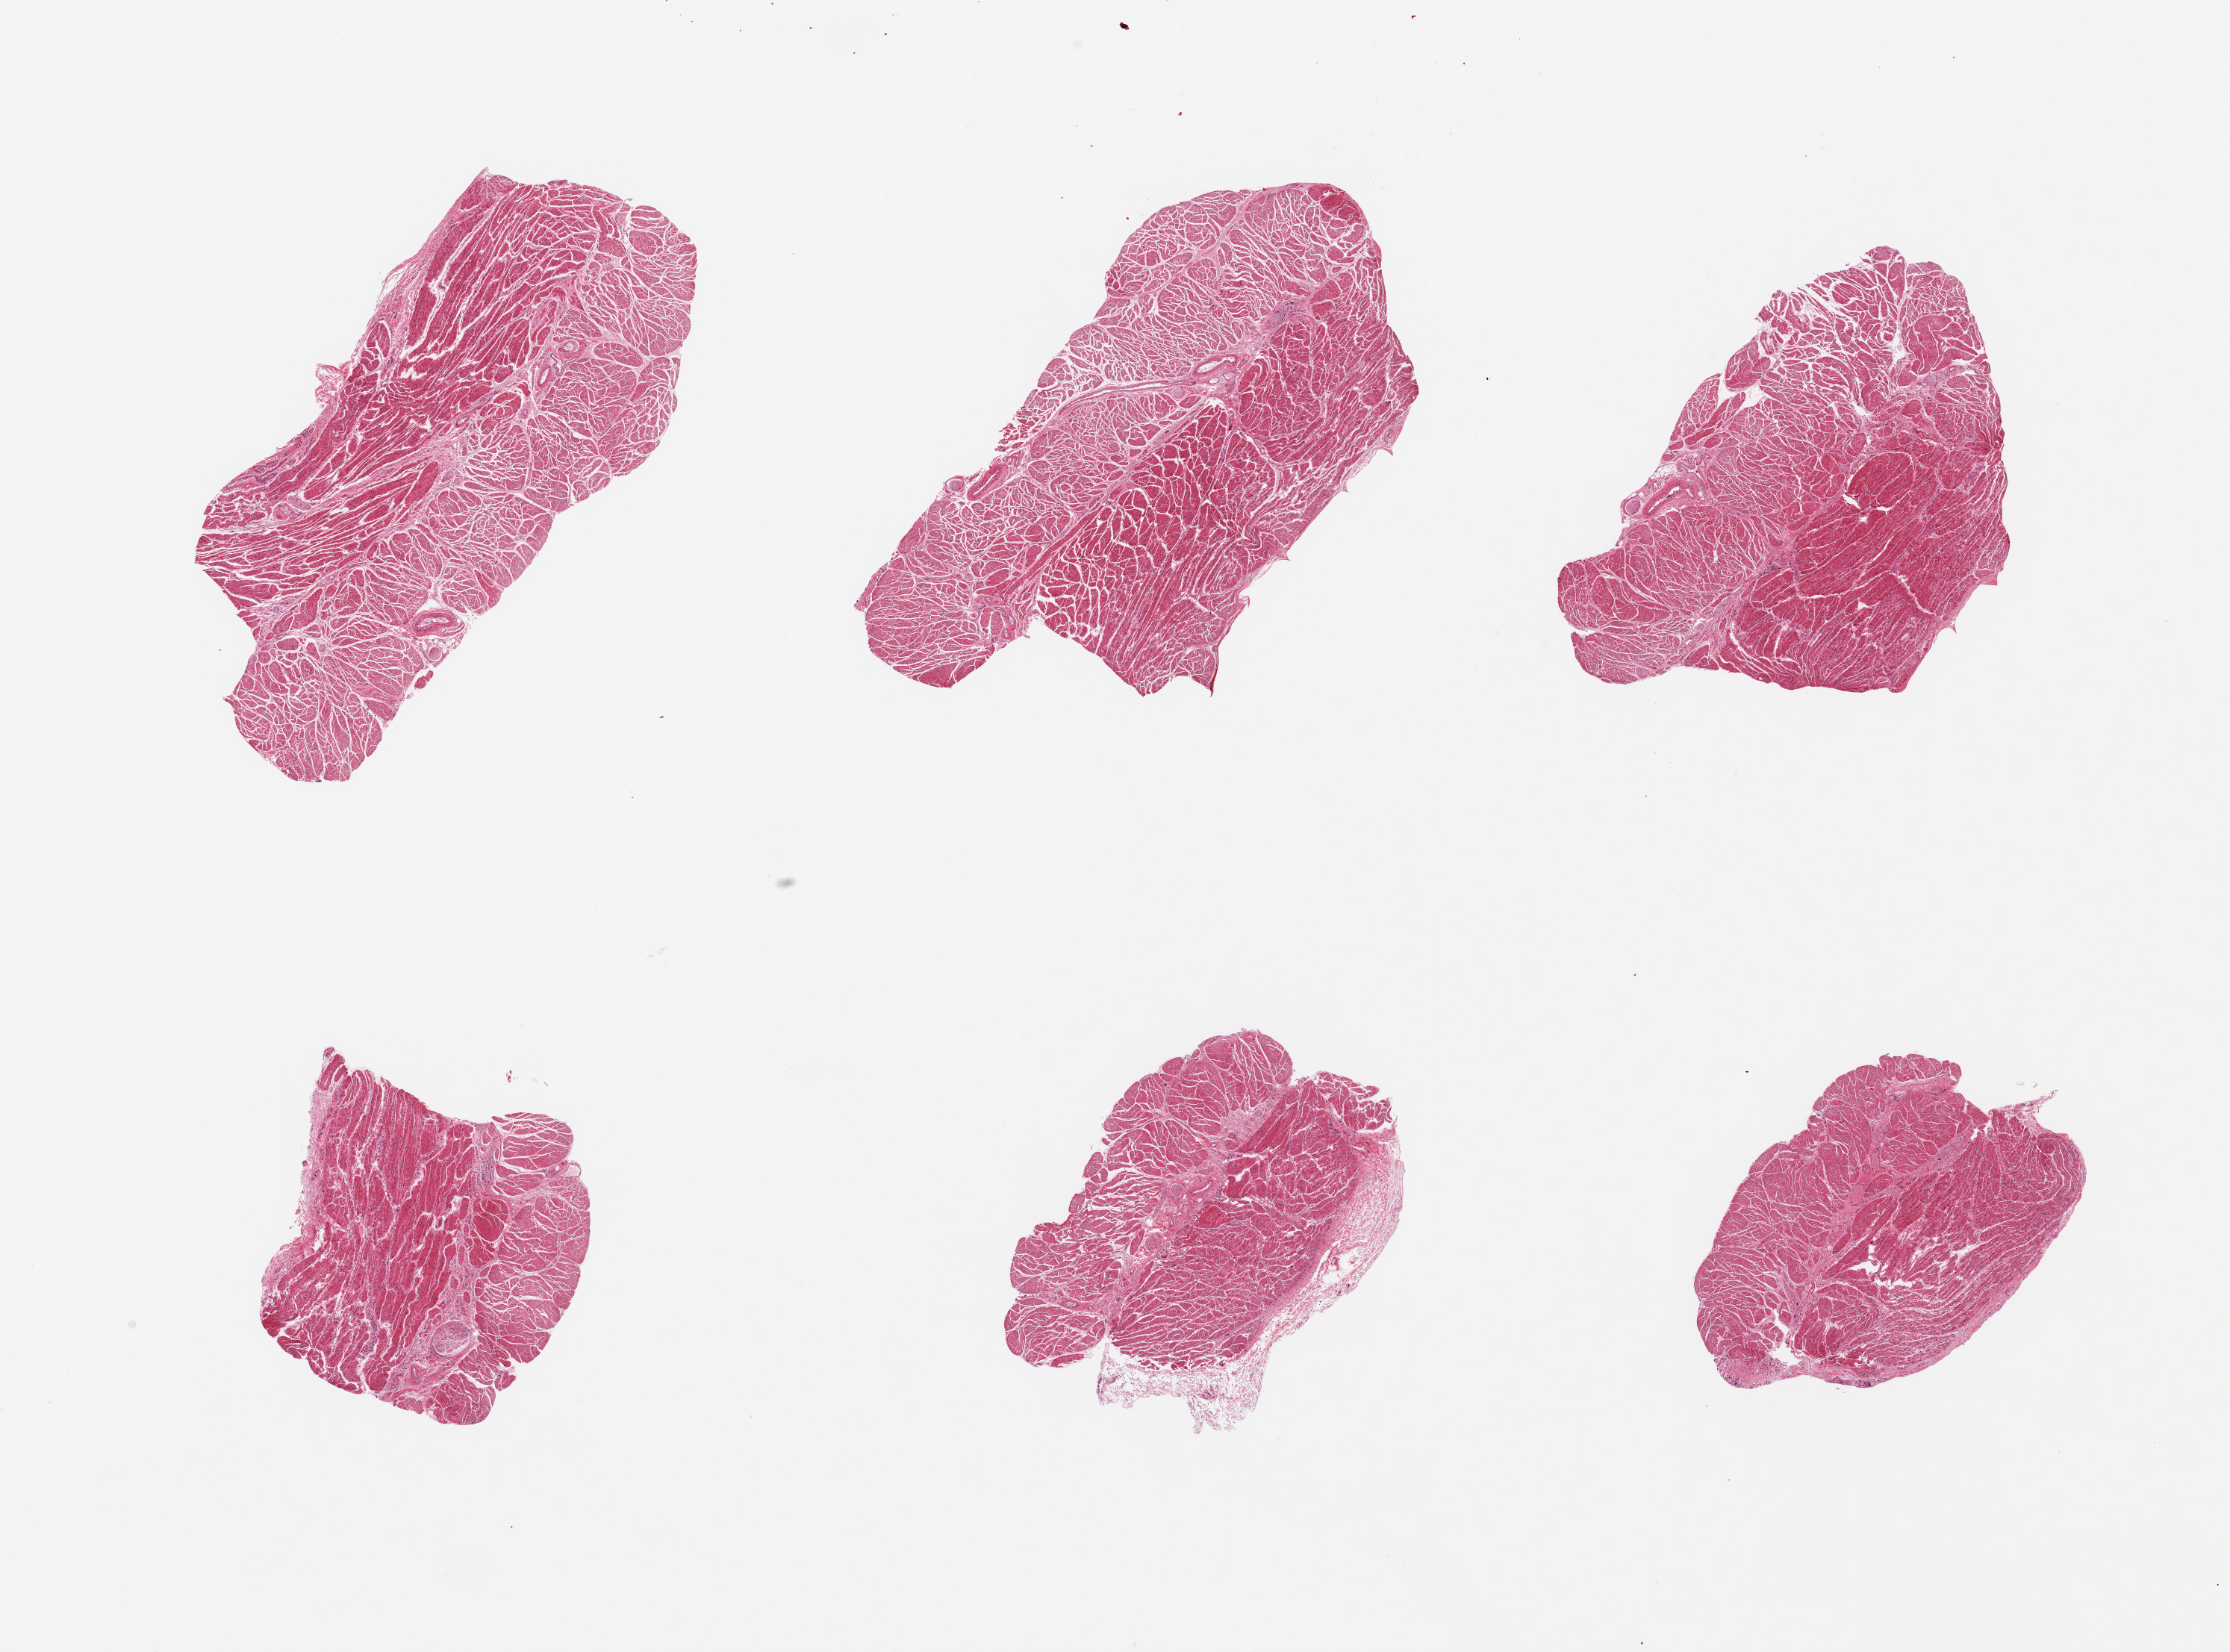
H&E whole-slide image, low-resolution overview of the scanned area, about 23.6 x 17.5 mm (acquisition: 20x scan). PAXgene-fixed paraffin-embedded (PFPE) section. Section of esophageal muscle (target tissue). Tissue donor sample. Donor: female.
* pathologist's review note for this sample: 6 pieces; muscularis